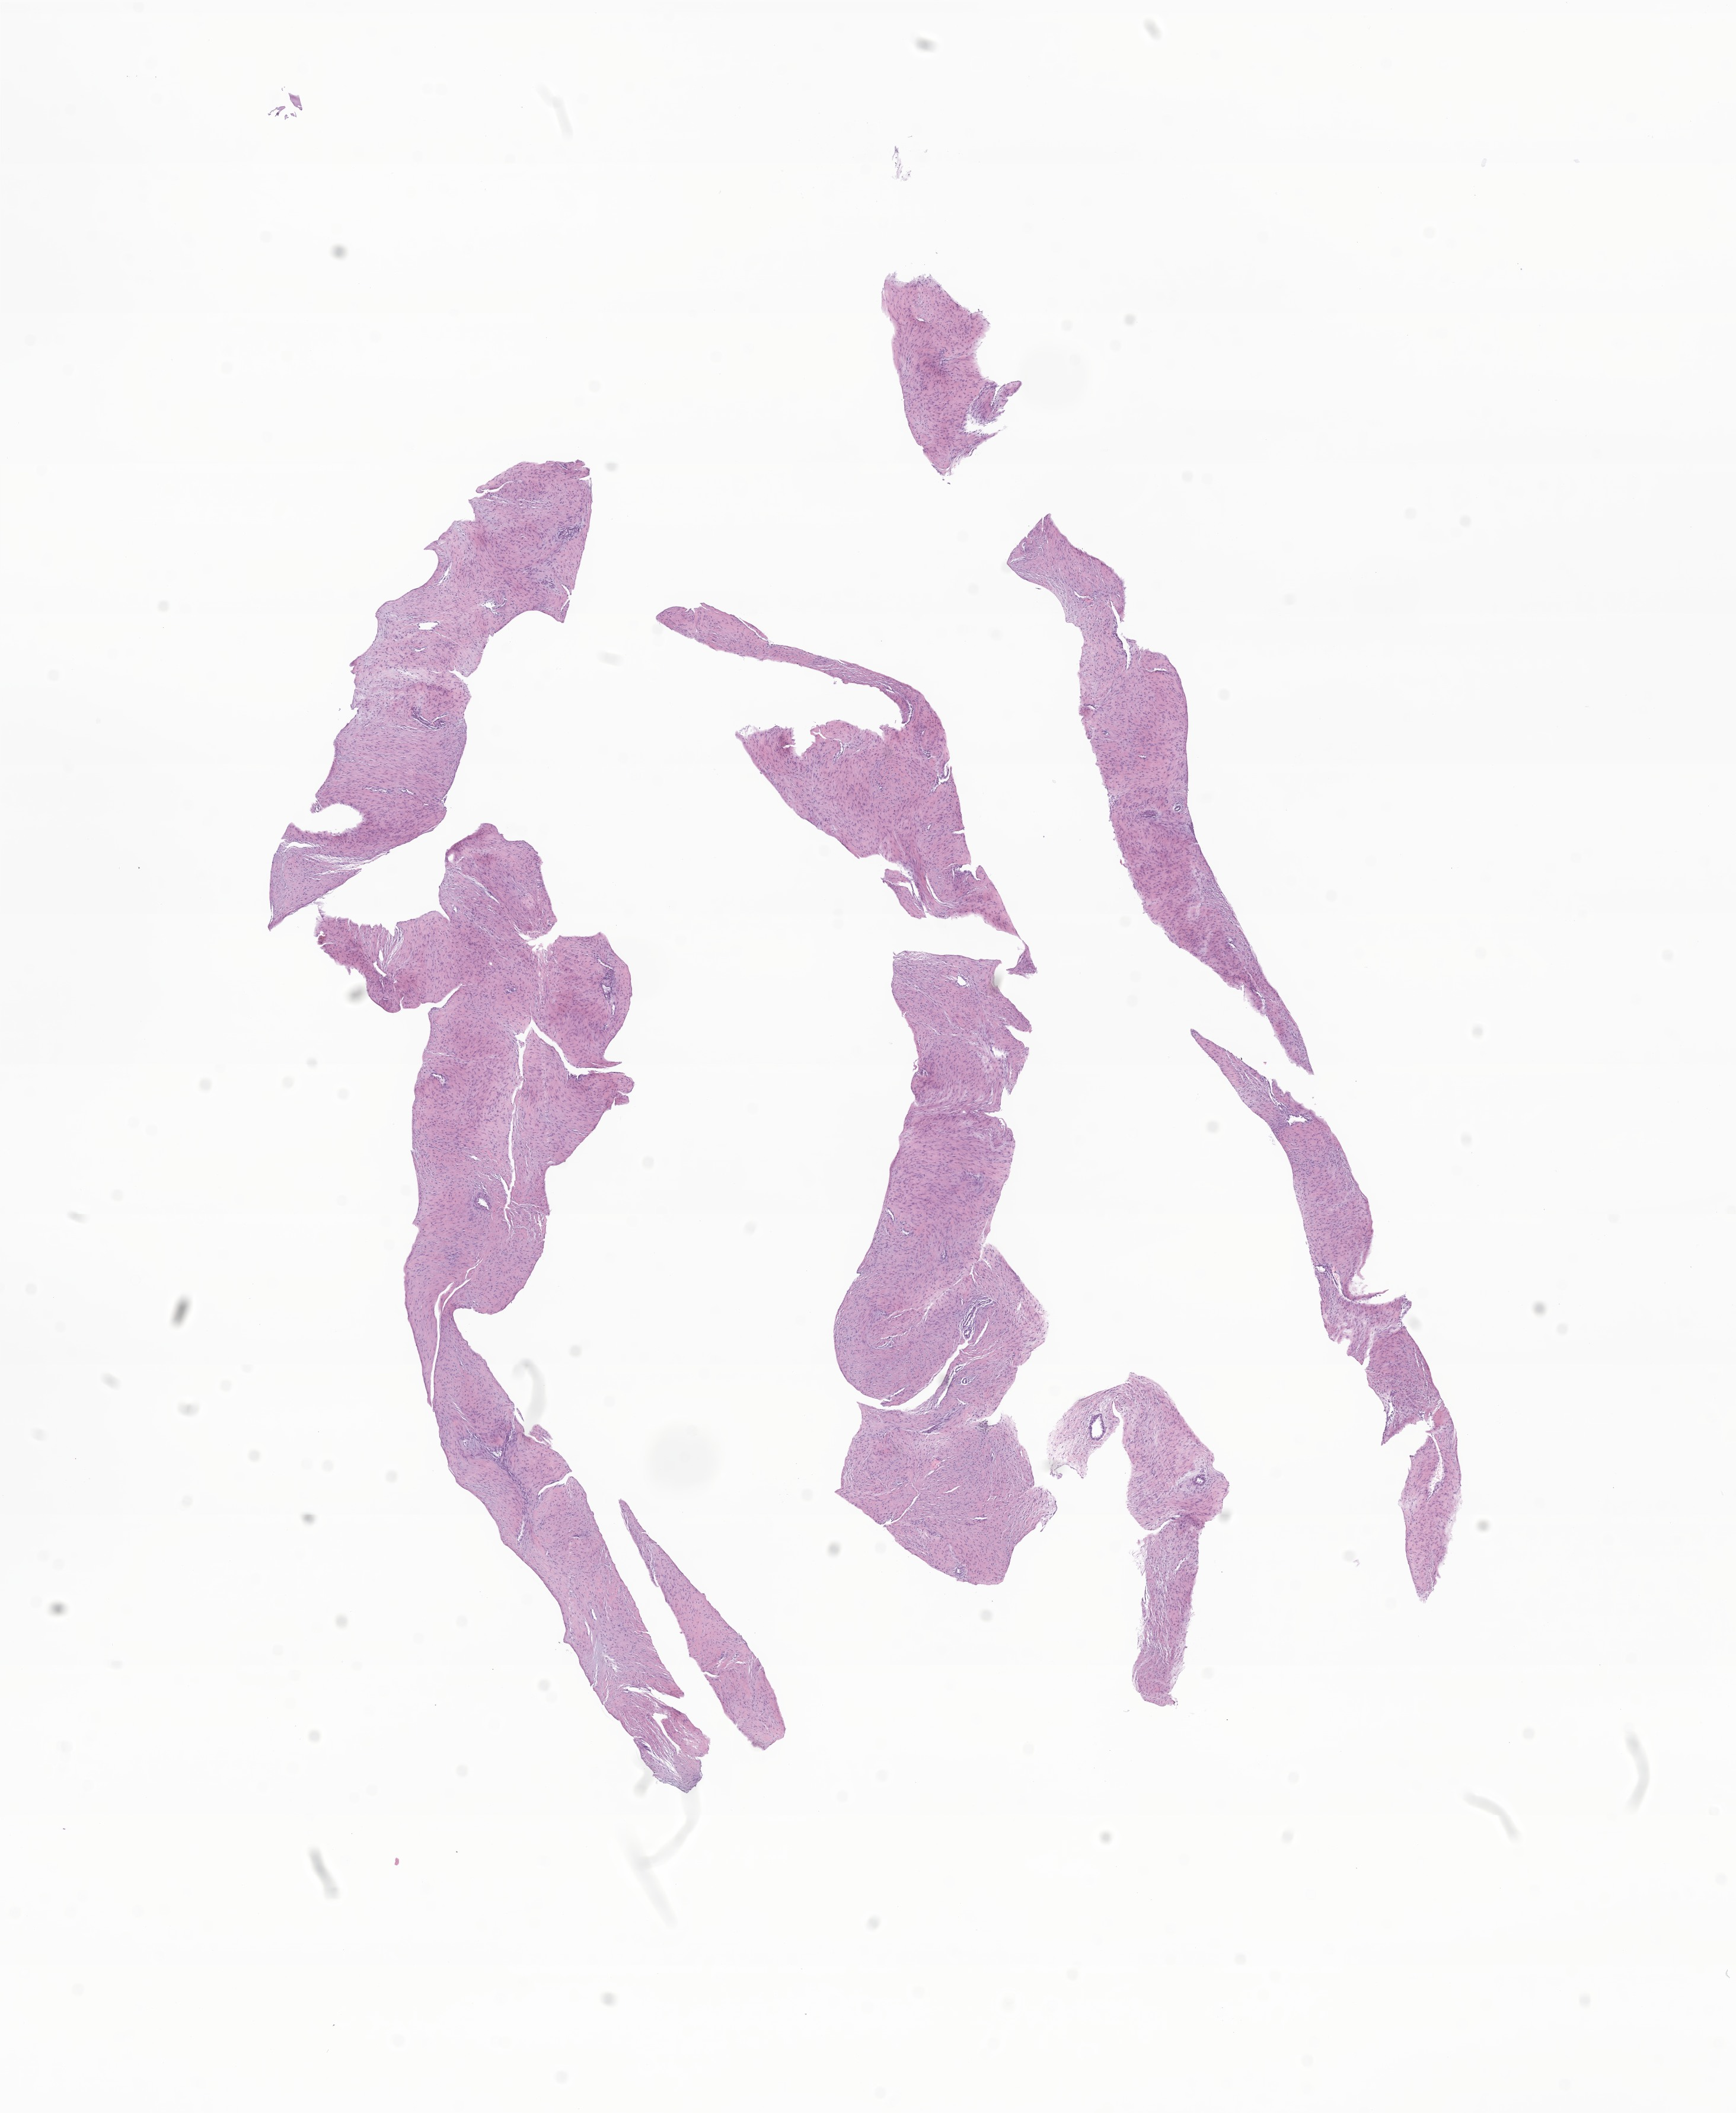
Digitized hematoxylin and eosin (H&E)-stained section of tumor tissue from the soft tissue of thorax, a low-resolution overview of the entire scanned area, about 12.3 x 15.0 mm; formalin-fixed paraffin-embedded section. Patient: female, age 197 months.
Diagnosis: Spindle cell sarcoma.